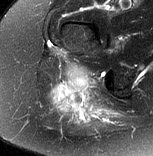
MRI of an extremity soft-tissue mass, one axial slice. Slice 53 of 77 in the series (ordered by position). T2-weighted fat-saturated. MR volume resampled by the dataset authors to the PET/CT grid (not the native acquisition matrix). 153 × 156 image matrix, field of view 149 × 152 mm. Female patient. From the clinical record (not read from this slice): histological type: synovial sarcoma; grade: intermediate; site of the primary tumour: right buttock.
Structures marked on this image (expert contour drawn on MRI and transferred to this co-registered scan by the dataset authors):
- gross tumour volume including surrounding oedema: bounding box <51,68,120,123> (left, top, right, bottom; pixels)
- gross tumour volume (mass): <62,68,91,89>